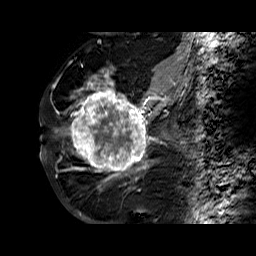
Breast MRI (dynamic contrast-enhanced), one sagittal slice. Dynamic contrast-enhanced series, time point 2 of 6 at this slice position (early post-contrast). 1.5 T. TE 6.3 ms, TR 32.4 ms. 4 mm slice thickness. 256 × 256 image matrix, field of view 200 × 200 mm. Female patient. Case-level facts recorded for this patient, not image findings: setting: breast cancer imaged before/during neoadjuvant chemotherapy; receptor status: HR-positive, HER2-negative.
Structures marked on this image (semi-automatic segmentation, software-assisted and operator-edited):
- analysis volume of interest (the breast-tissue region the enhancement analysis was run in; not a lesion): bounding box <68,72,177,182> (left, top, right, bottom; pixels)
- tumour enhancement mask (voxels above the 100 % enhancement threshold inside the analysis volume of interest): <70,74,175,181>